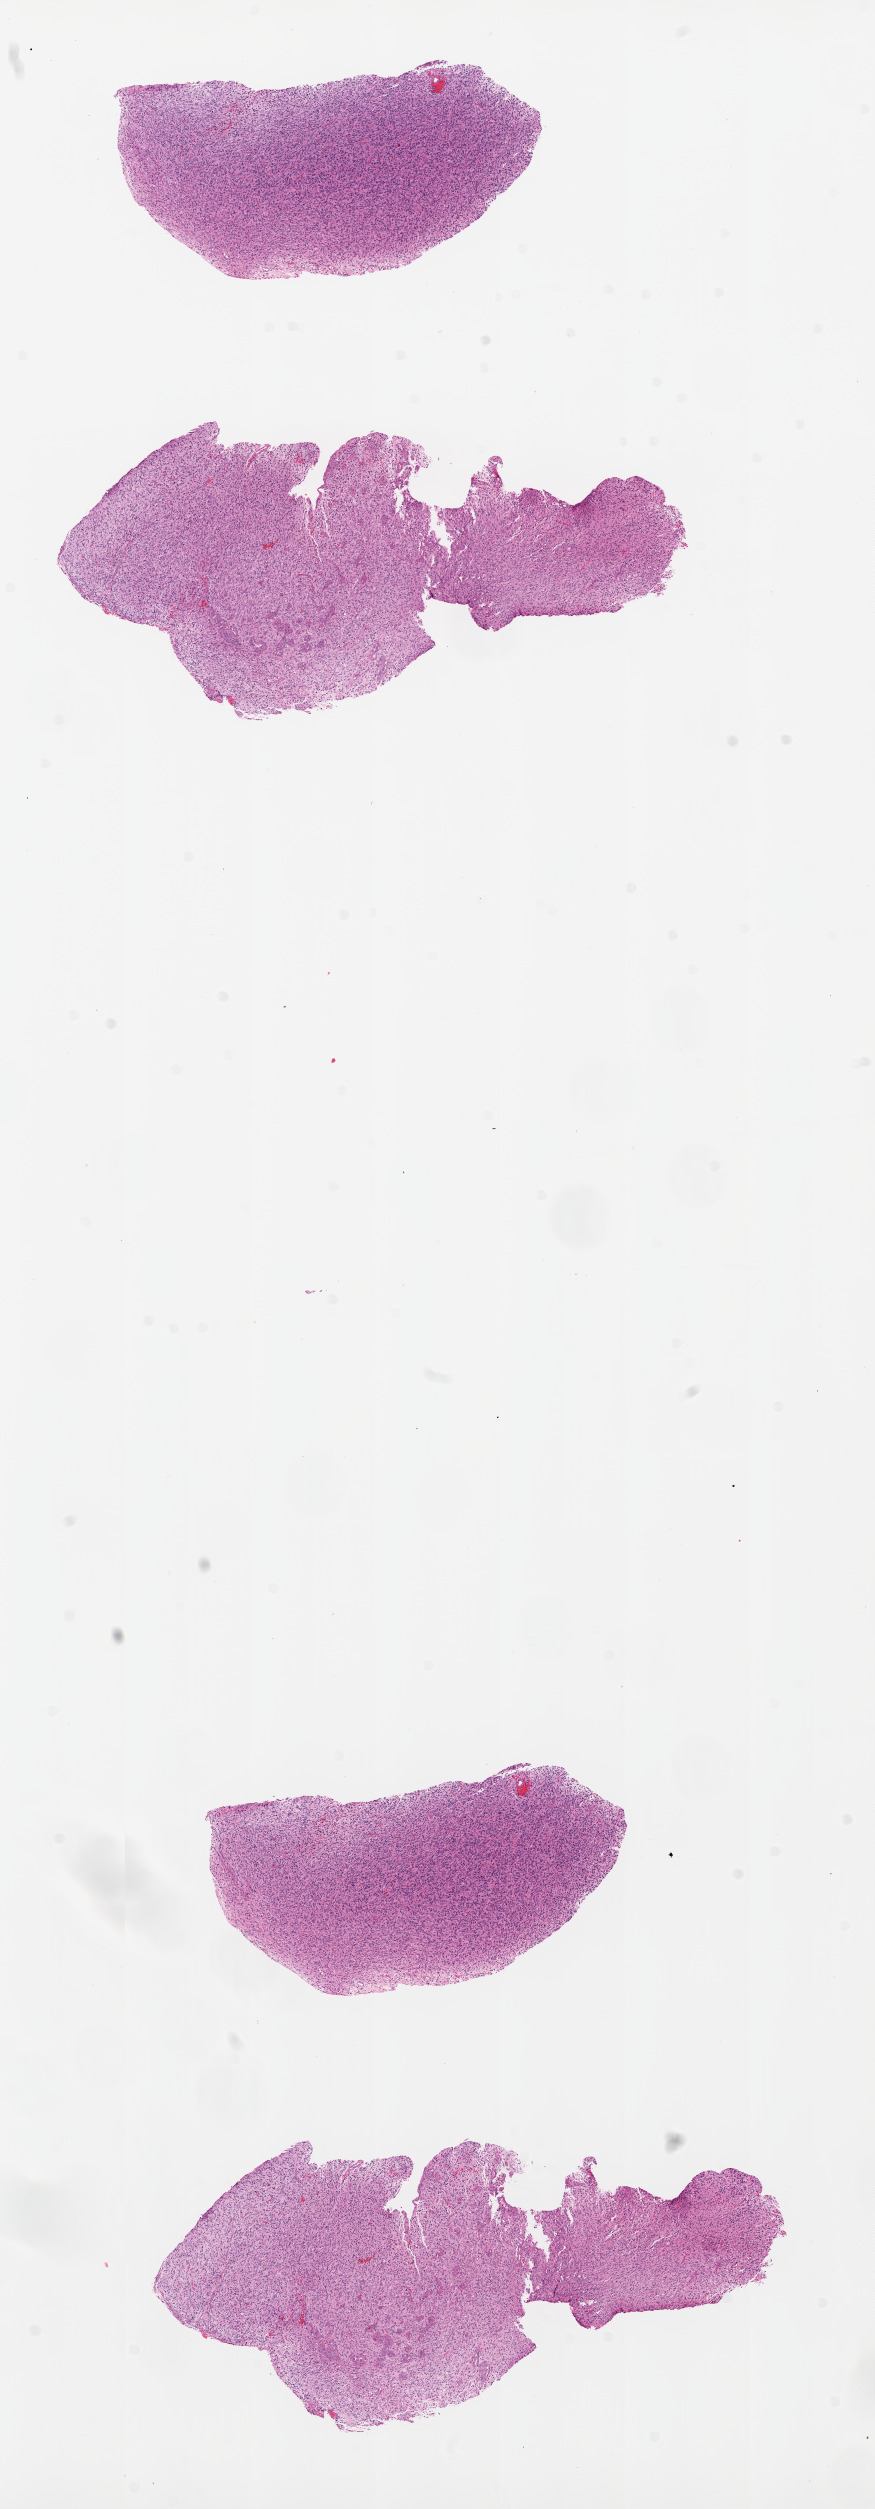
Whole-slide histology image, H&E, low-resolution overview of the scanned area, about 7.0 x 20.1 mm (acquisition: 20x scan). Formalin-fixed paraffin-embedded (FFPE) diagnostic section. Brain, primary tumour sample. Patient: male, age at initial diagnosis 73 years.
Histologic diagnosis: Glioblastoma.